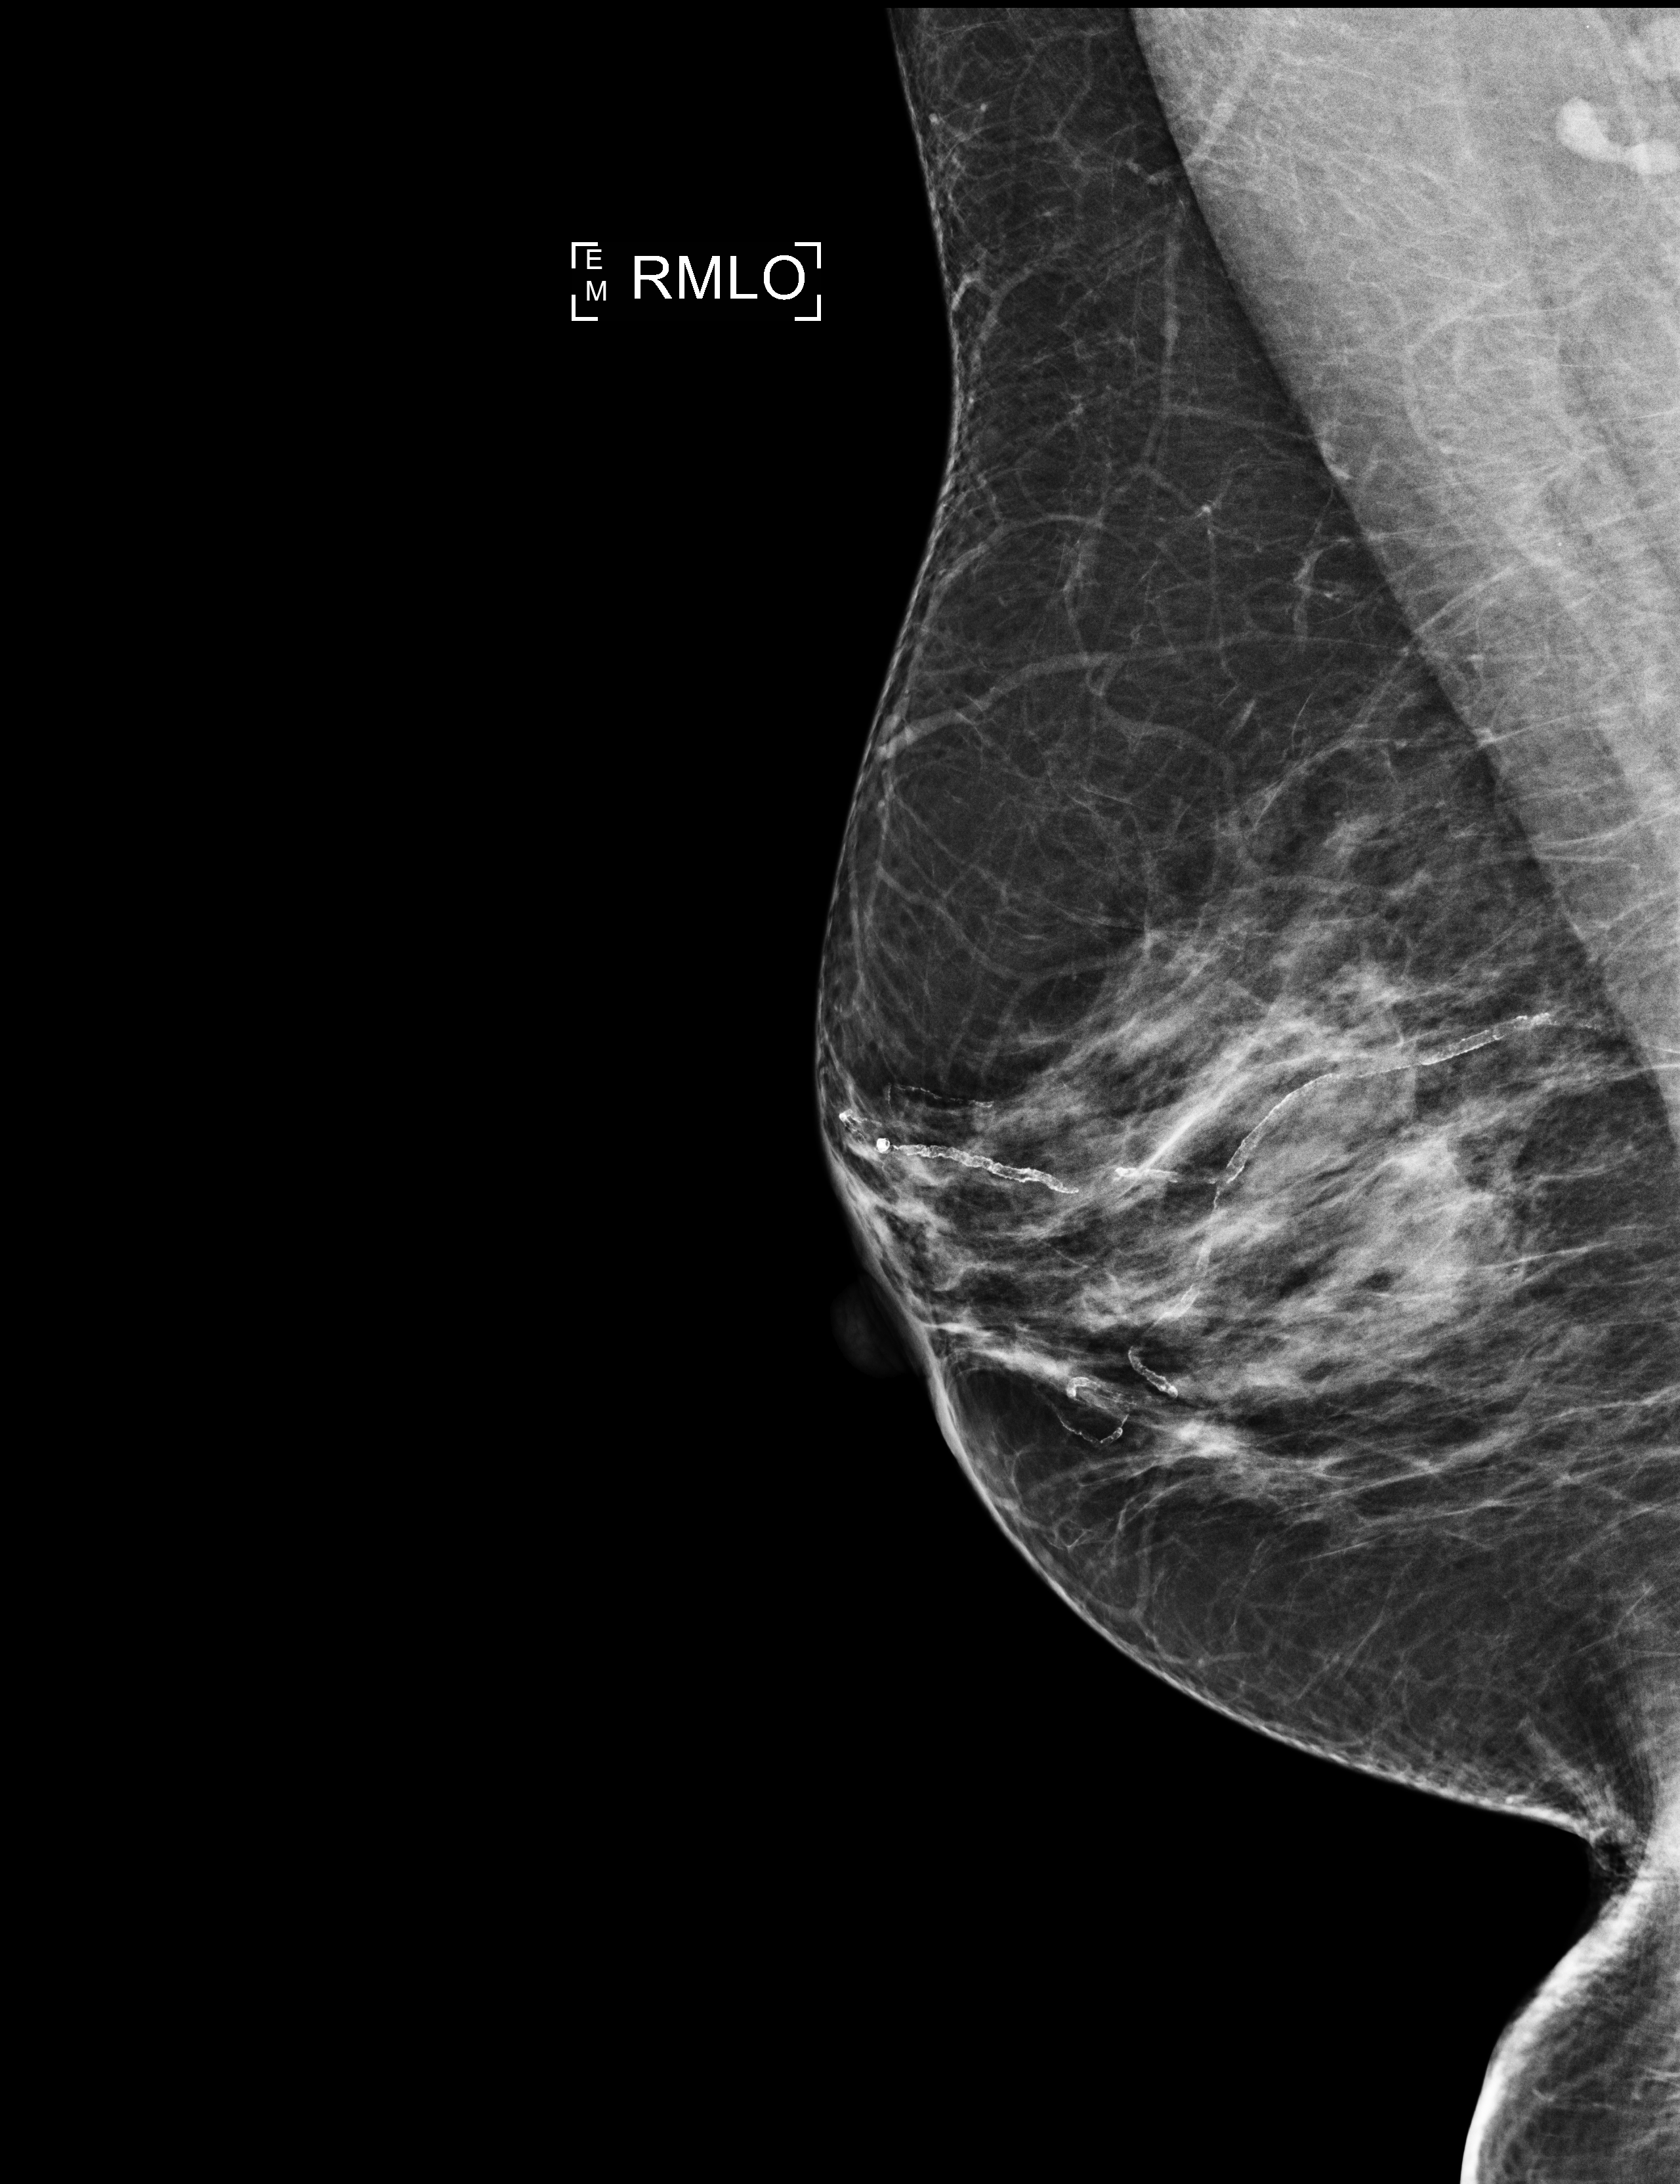
Digital mammogram (FFDM); right breast; mediolateral oblique (MLO) view; screening examination. Female patient, age 59 years.
Final BI-RADS category for the screening round (tomosynthesis exam, both breasts): category 1.